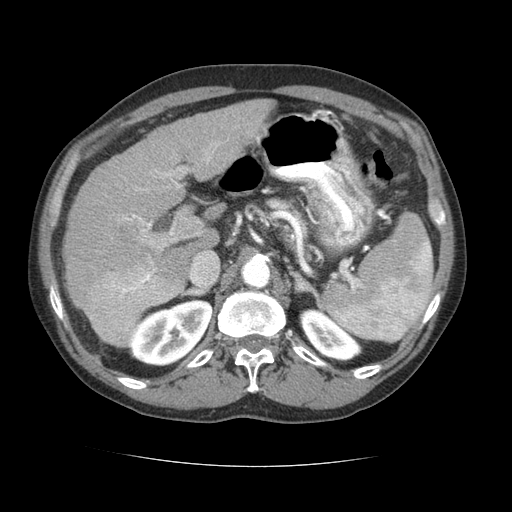
Contrast-enhanced abdominal CT (liver protocol), one axial slice; position 44 of 69 along the scan axis; reconstruction kernel STANDARD; soft-tissue window (W 400 / L 40 HU); 512 × 512 image matrix, field of view 360 × 360 mm. From the clinical record (not read from this slice): diagnosis: hepatocellular carcinoma (patient treated with transarterial chemoembolisation; whether this scan precedes or follows treatment is not stated here); TNM stage (as recorded): Stage-II; Child-Pugh class: B; tumour nodularity: multinodular.
Structures marked on this image (semi-automatically segmented with operator editing):
- liver parenchyma outside the tumour (the mass and vessels are separate outlines, so this box may not span the whole liver): box from (x=62, y=98) to (x=274, y=344) px
- mass: (x=84, y=269)–(x=184, y=347)
- liver vessels: (x=122, y=143)–(x=219, y=270)